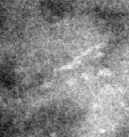
Cropped region of a digitized screen-film mammogram centred on a radiologist-marked abnormality; right breast; MLO view; BI-RADS breast density category 2 (scale 1–4).
Marked abnormality: calcifications, morphology pleomorphic / fine linear branching, distribution segmental; BI-RADS assessment category 5; pathology (as recorded): malignant.